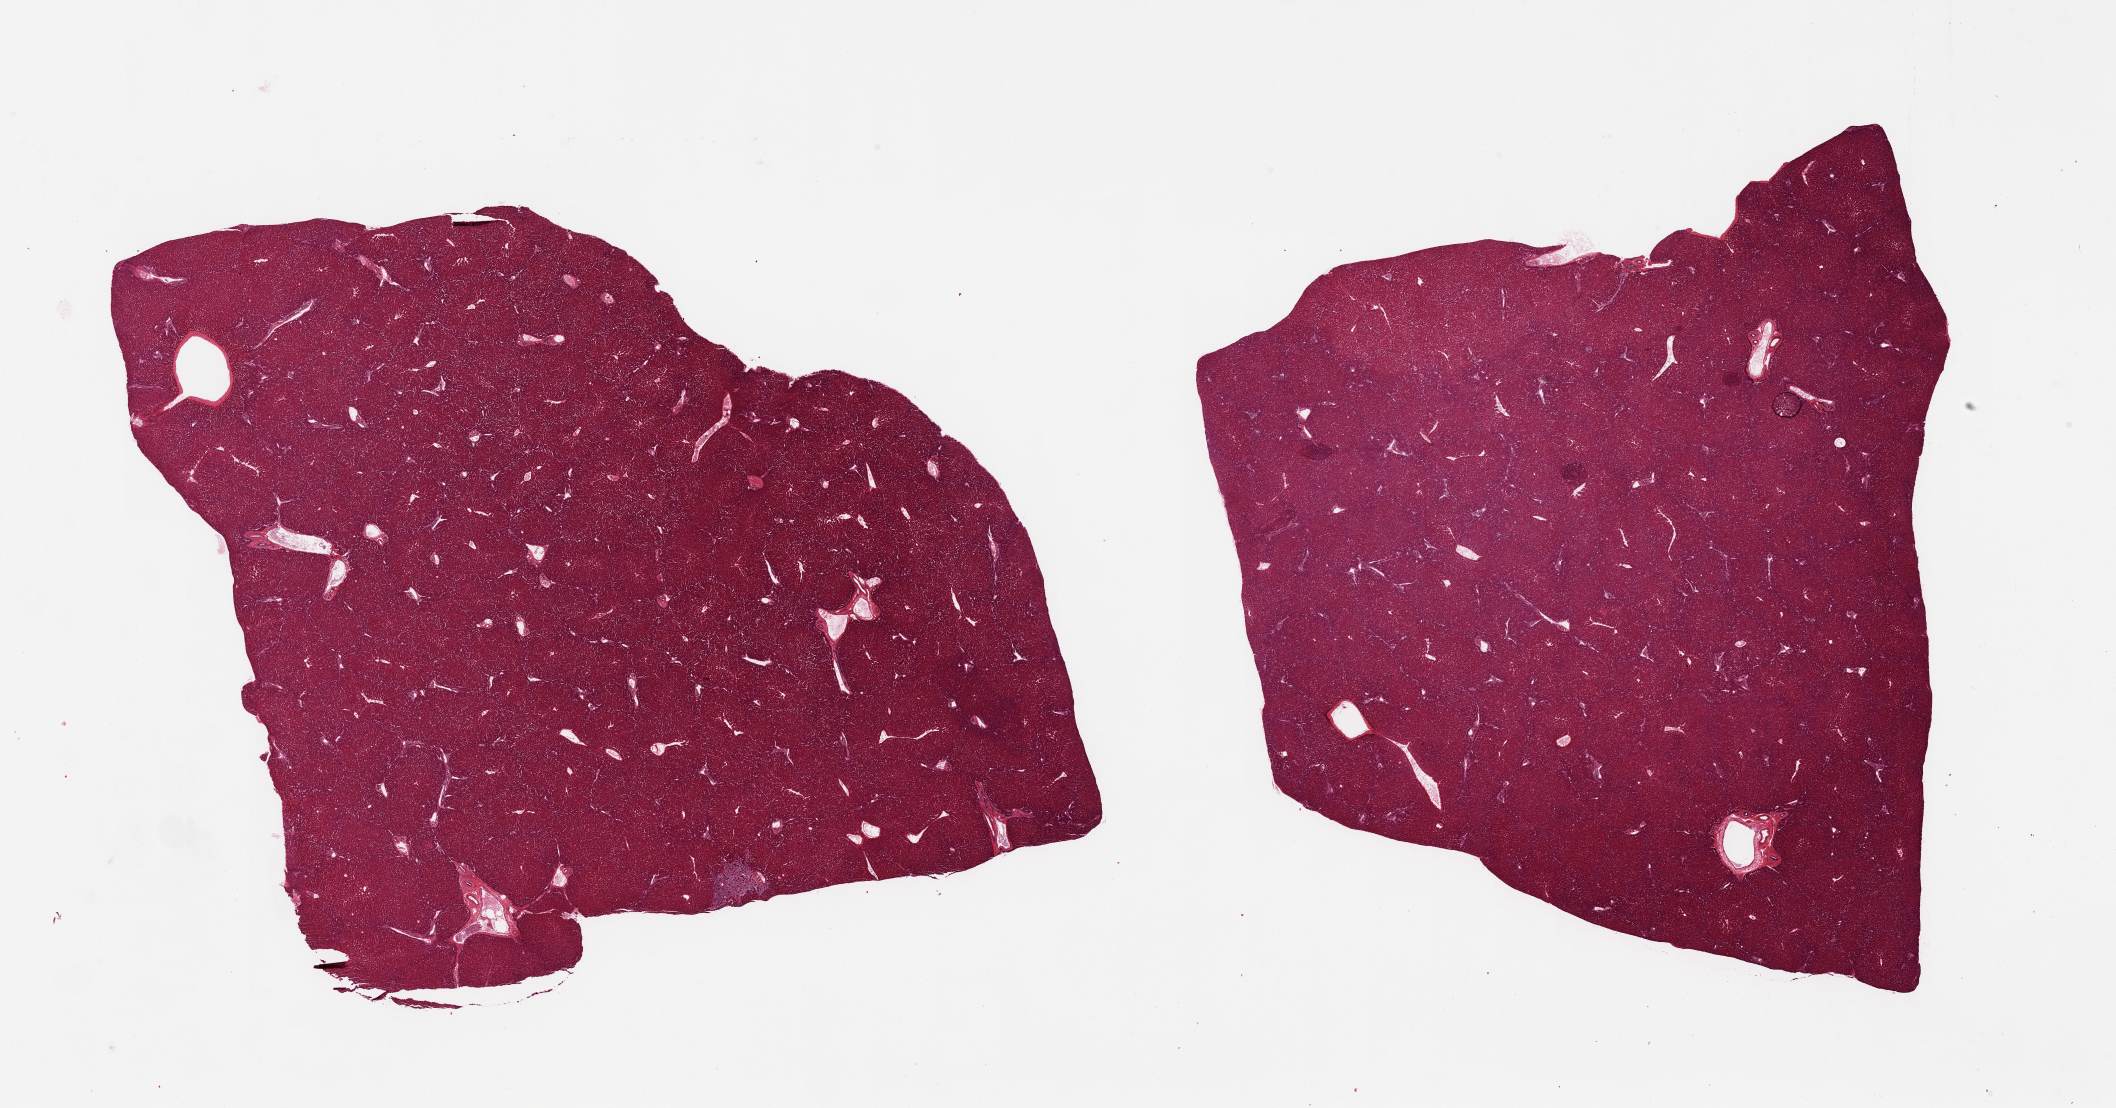
Whole-slide image, hematoxylin and eosin (H&E) stain — whole scanned area (about 33.5 x 17.5 mm) shown as a low-resolution overview. PAXgene-fixed, paraffin-embedded tissue. Target tissue: liver. Donor tissue sample. Donor: male.
- review note (as recorded): 2 pieces